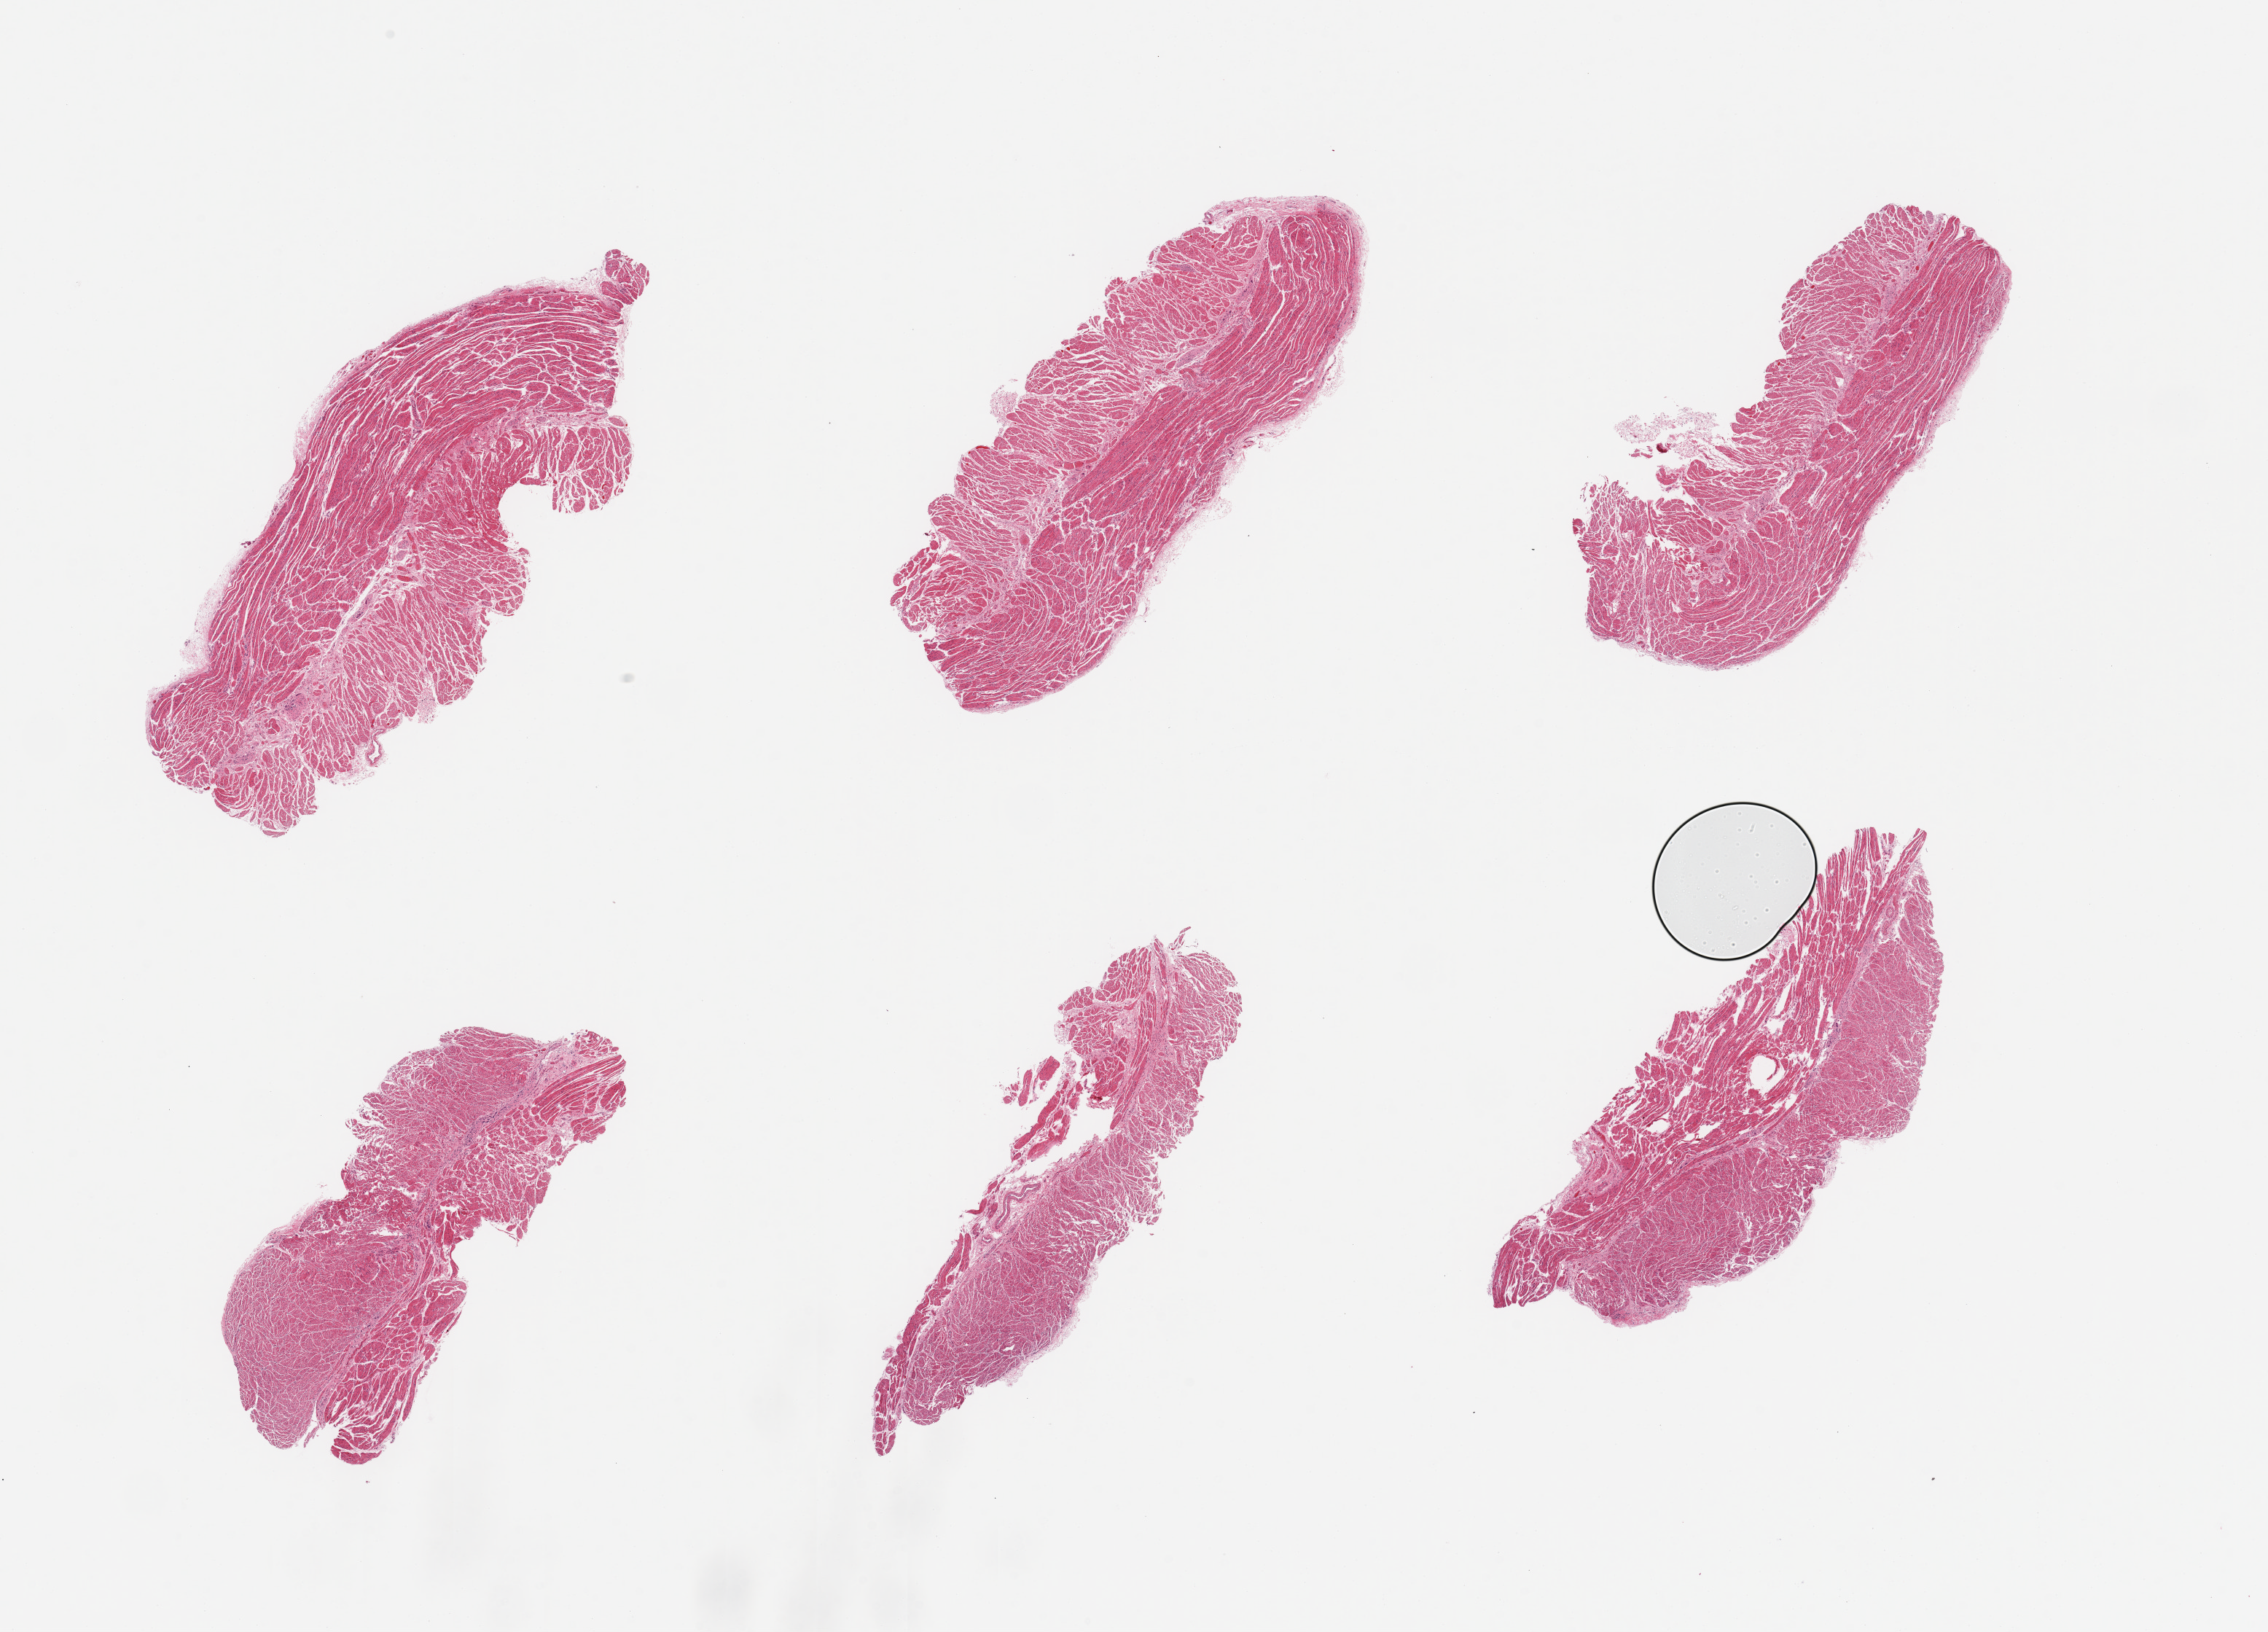
Digitized hematoxylin and eosin (H&E)-stained section — whole scanned area (about 24.6 x 17.7 mm) shown as a low-resolution overview. PAXgene-fixed, paraffin-embedded tissue. Target tissue: esophageal muscle. Tissue donor sample. Male donor.
Review note (as recorded): 6 pieces; well dissected.